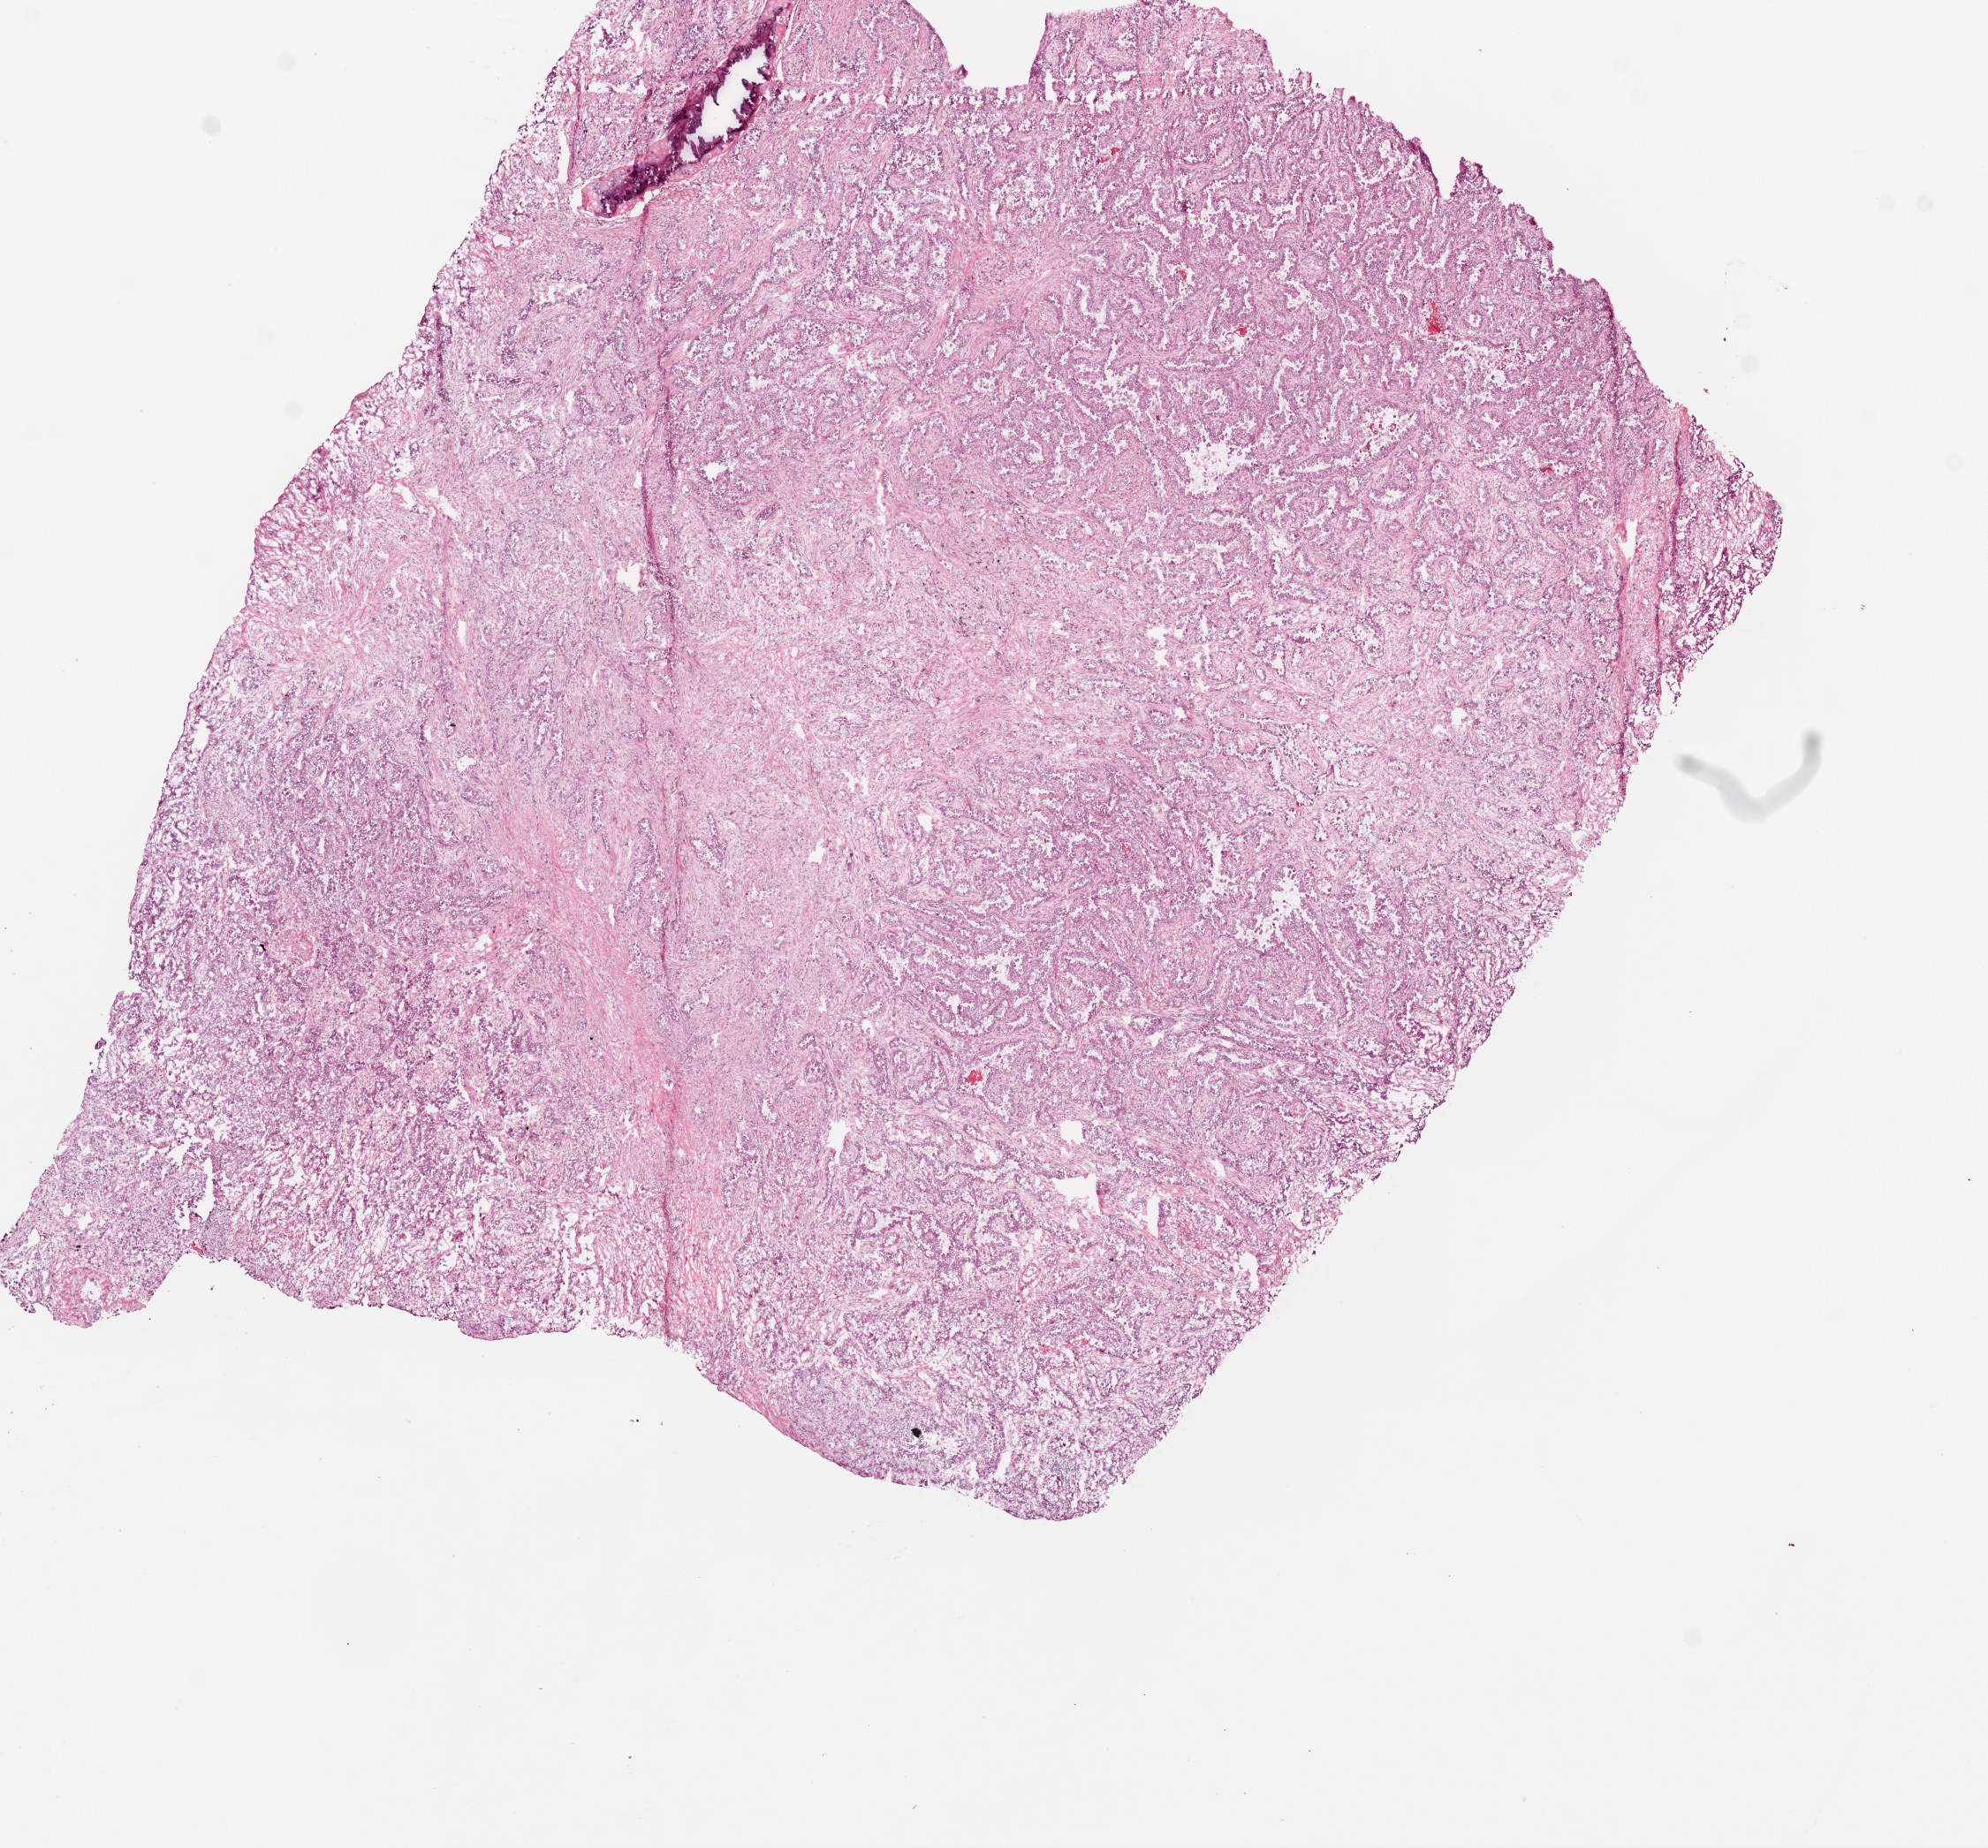
Digitized Hematoxylin and eosin (H&E) stained tissue section (whole slide) — a low-resolution overview of the entire scanned area, about 9.0 x 8.4 mm. Frozen section. Primary tumour sample from the lung. Female, age 65 years at initial diagnosis. Pathologist review of this section (percent, as recorded): tumour cells 84%, tumour nuclei 75%, normal cells 0%, stromal cells 15%, necrosis 1%.
Histologic diagnosis: Adenocarcinoma, NOS (upper lobe, lung). AJCC pathologic stage: IIB (5th edition).